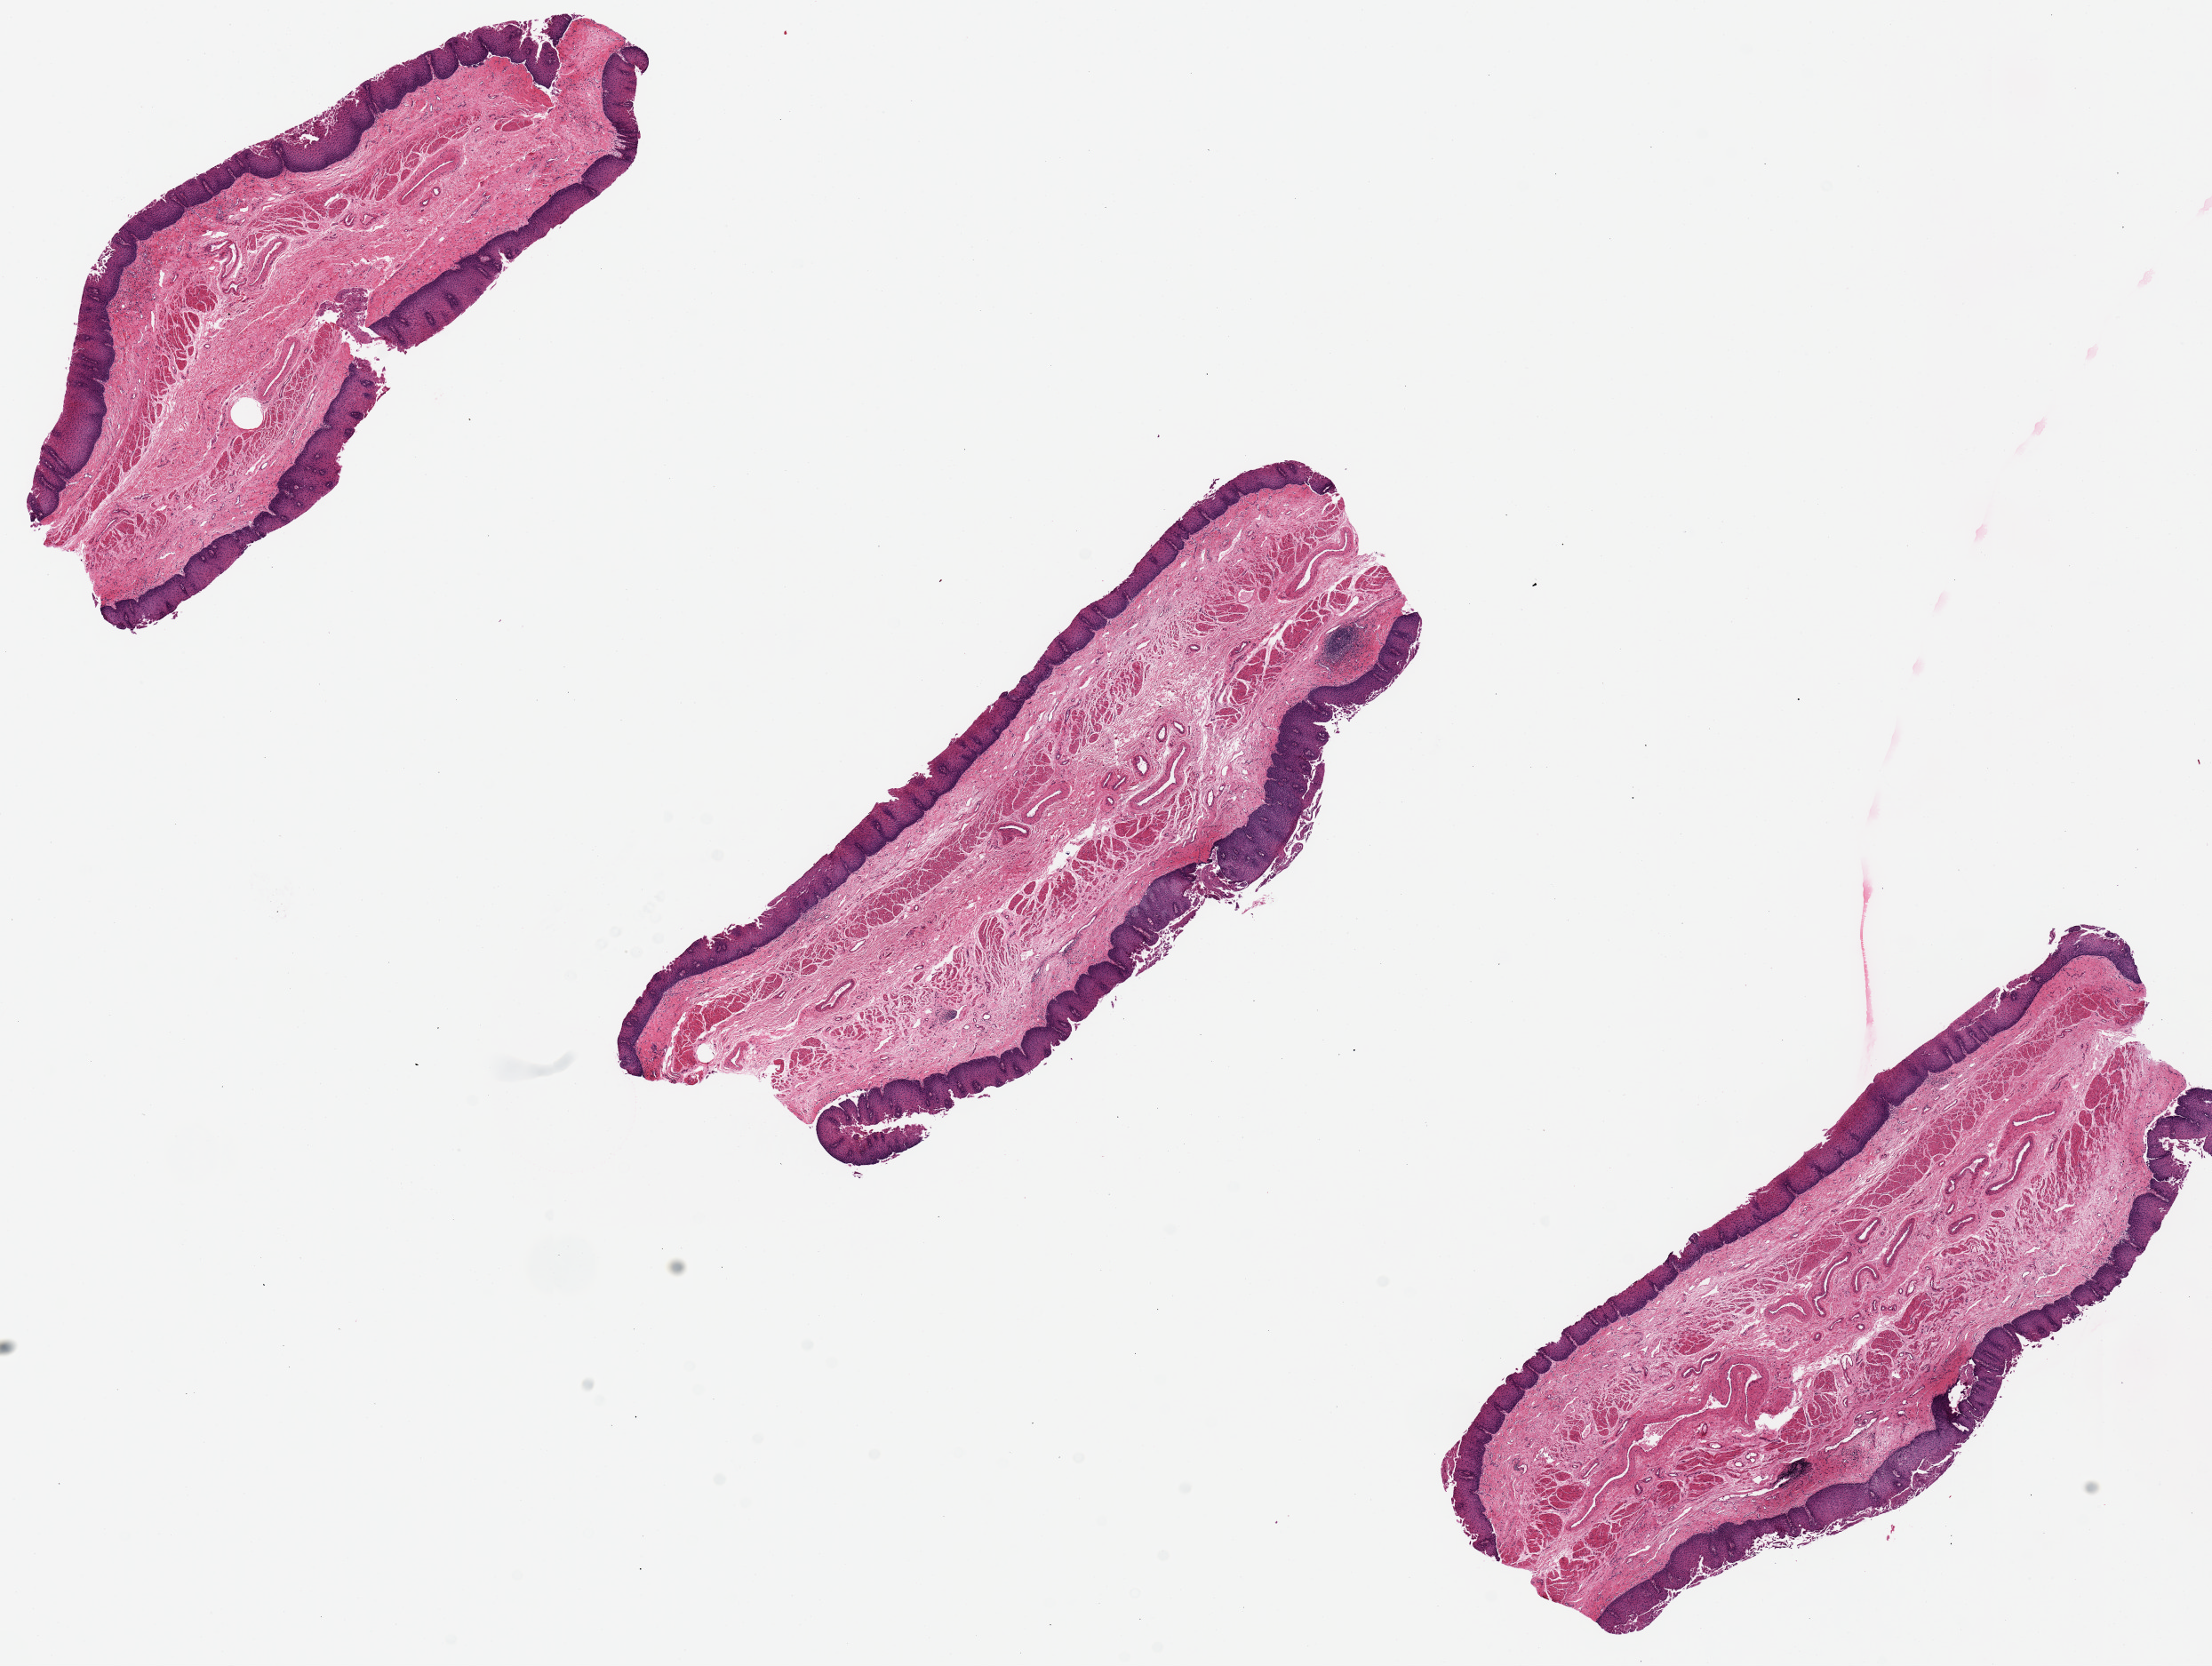
Digitized H&E-stained section, low-resolution overview of the scanned area, about 19.7 x 14.8 mm; PAXgene-fixed, paraffin-embedded tissue; section of esophageal mucous membrane (target tissue); donor tissue sample. Male donor.
• review note (as recorded): Mucosa is ~15-20% total thickness